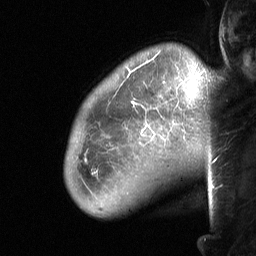
Breast MRI (dynamic contrast-enhanced), one sagittal slice. Dynamic contrast-enhanced study with each time point stored as its own series, time point 2 of 3 at this slice position (early post-contrast, ordered by acquisition time). 1.5 T. TE 4.8 ms, TR 27 ms. 256 × 256 image matrix. Patient: female, 50 years. Case-level facts recorded for this patient, not image findings: setting: breast cancer imaged before/during neoadjuvant chemotherapy; receptor status: HER2-positive.
Structures marked on this image (semi-automatically segmented with operator editing):
- analysis volume of interest (the breast-tissue region the enhancement analysis was run in; not a lesion): bounding box [x1, y1, x2, y2] px = [65, 62, 222, 222]
- tumour enhancement mask (voxels above the 90 % enhancement threshold inside the analysis volume of interest): [92, 101, 133, 174]